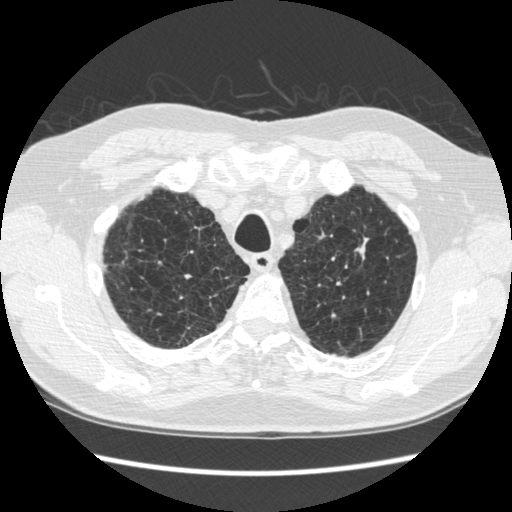
Axial slice from a low-dose chest CT screening exam. Second annual screen. Lung window (W 1500 / L -600 HU). 1.25 mm slice thickness. Standard (soft-tissue) reconstruction kernel (STANDARD). Slice 50 of 295 in the series. 512 × 512 image matrix, field of view 348 × 348 mm. Male, age 70 years at enrolment. Former smoker at enrolment.
Expert-annotated lung lesion, box from (x=333, y=215) to (x=394, y=282) px. The screening reader recorded 5 non-calcified nodules or masses ≥4 mm on this exam (right lower lobe, right lower lobe, right lower lobe, left upper lobe, left lower lobe); which of them this box marks is not recorded. Official screen result: positive, change unspecified: nodule(s) >= 4 mm or enlarging nodule(s), mass(es), or other non-specific abnormalities suspicious for lung cancer.